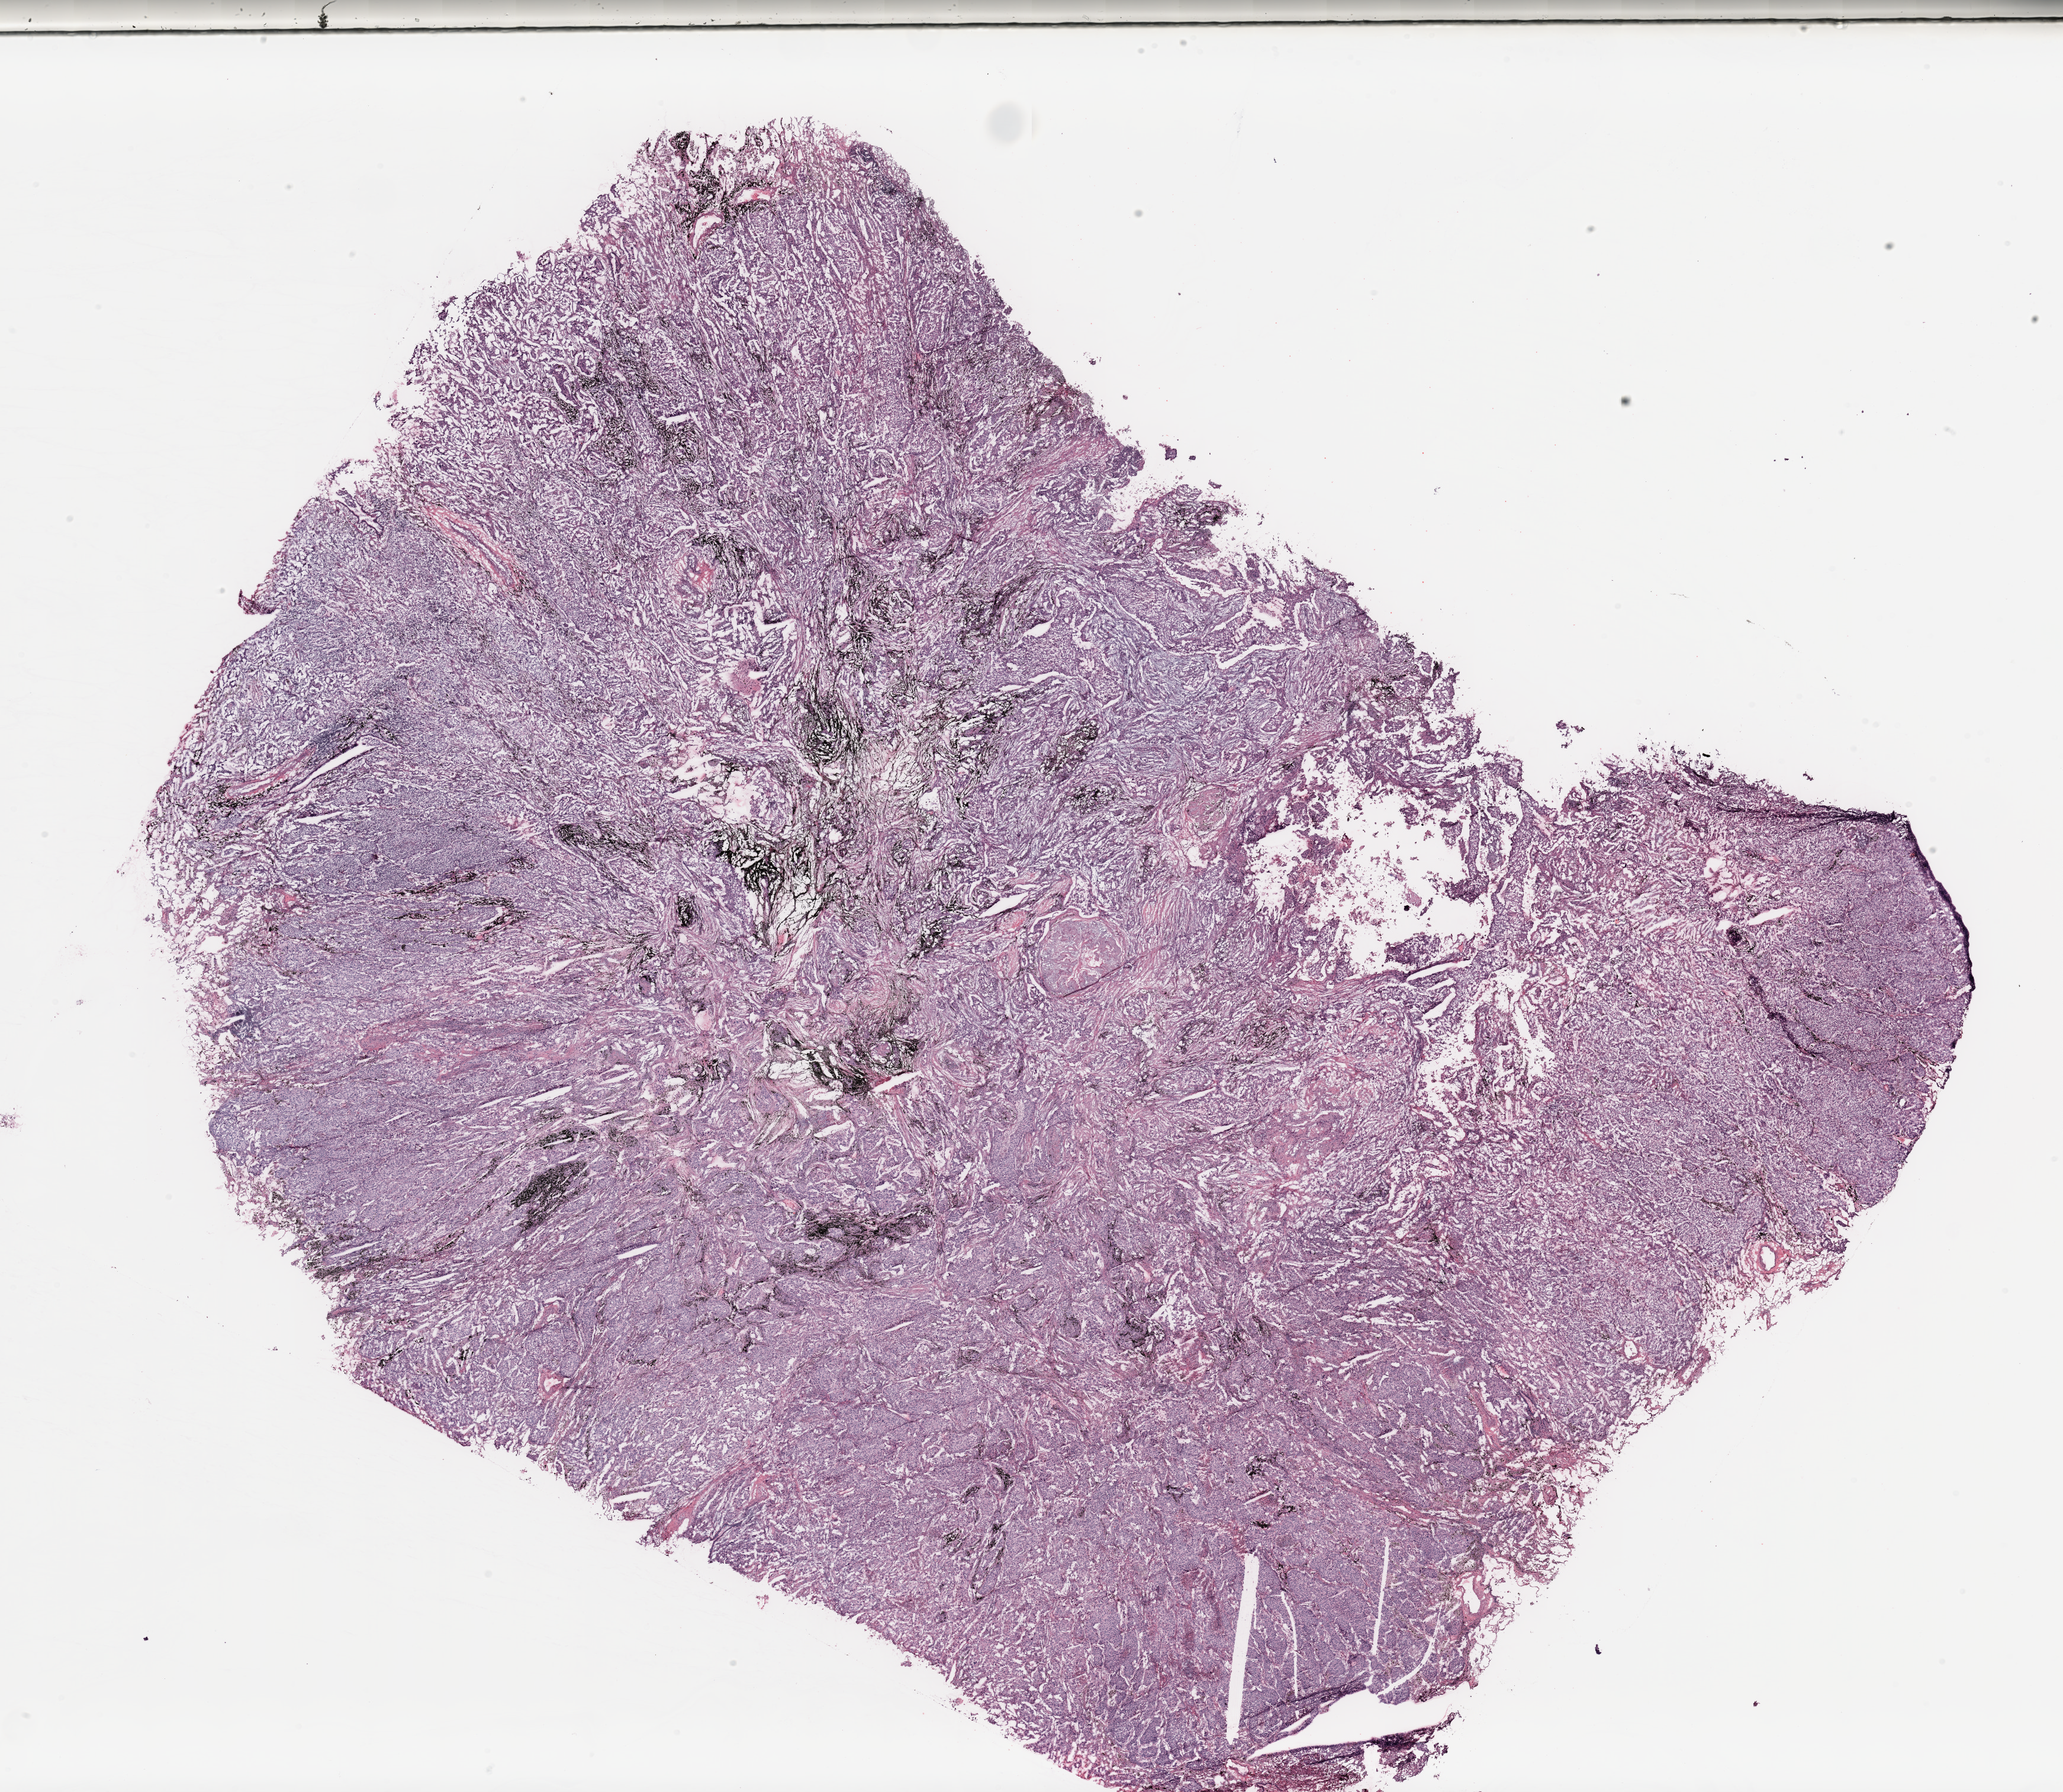
Digitized H&E-stained tissue section (whole slide) — a low-resolution overview of the entire scanned area, about 27.6 x 23.9 mm (from a 20x scan); tumour tissue sample, sampled site: lung. 62-year-old male patient. Histologic grade: GX (grade cannot be assessed). Composition of this section per pathologist review: tumour nuclei 80%, necrosis 5%.
Diagnosis: Adenocarcinoma, NOS. AJCC pathologic stage: IIIA.